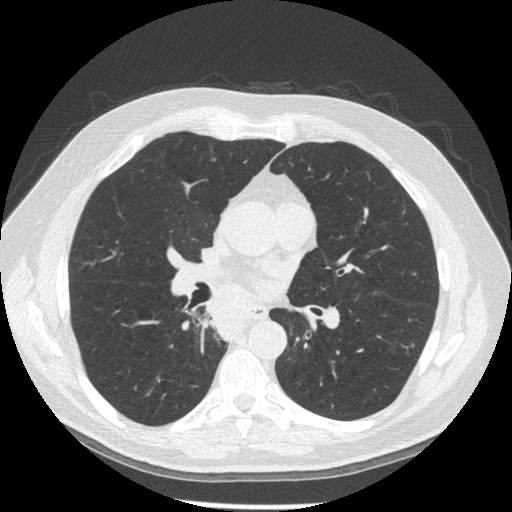
Low-dose screening chest CT, axial slice; third annual screen; lung window (W 1500 / L -600 HU); 1.25 mm slice thickness. Male participant, aged 61 years at enrolment. Former smoker at enrolment.
Expert reader's lesion annotation, bounding box (x1, y1, x2, y2) in pixels: (204, 298, 255, 347). Screening reader's record for this exam: no non-calcified nodule ≥4 mm recorded. Official screen result: positive, other. Participant outcome: lung cancer diagnosed 10 days after this screen — squamous cell carcinoma, keratinizing, NOS, right lower lobe, stage IIIB (AJCC 6th edition), 40 mm at pathology.